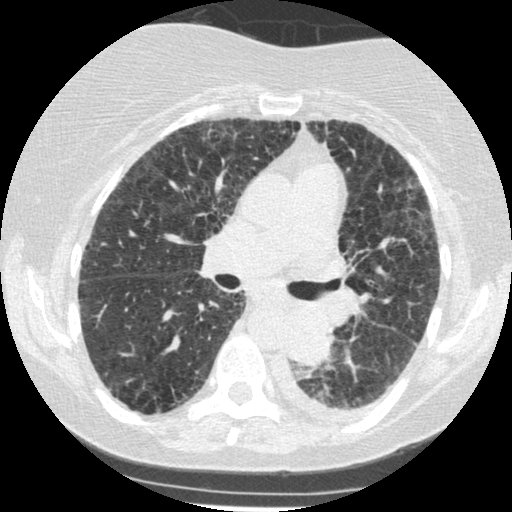
Low-dose screening chest CT, one axial slice. Slice 149 of 341 in the series (ordered by position). Reconstruction kernel STANDARD. Lung window (W 1500 / L -600 HU). 512 × 512 image matrix, field of view 310 × 310 mm.
Annotated regions visible in this slice (outlined manually by an expert reader):
- lesion 1 (tumor, lower lobe of left lung): bounding box [x1, y1, x2, y2] px = [287, 309, 334, 366]